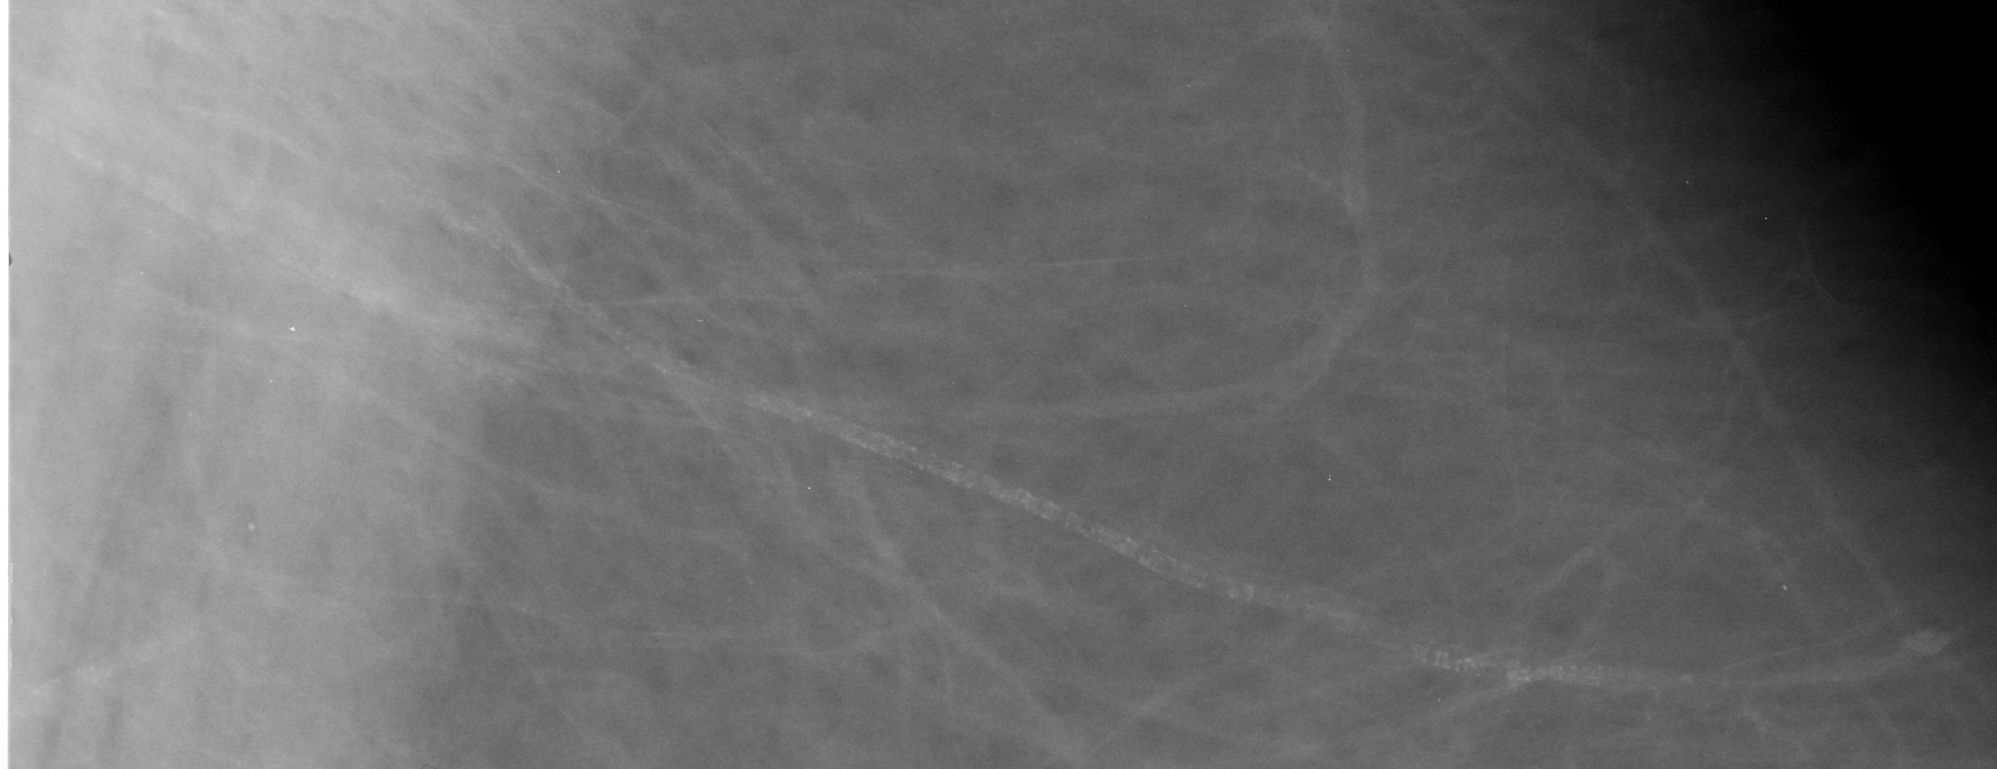
Crop from a digitized film mammogram around one marked abnormality; left breast; MLO view; BI-RADS breast density category 2 (scale 1–4).
Calcifications, morphology vascular / coarse / lucent centered; BI-RADS assessment category 2; subtlety rating 5 on a 1 (subtle) to 5 (obvious) scale; benign; no additional work-up was recommended (benign without callback).